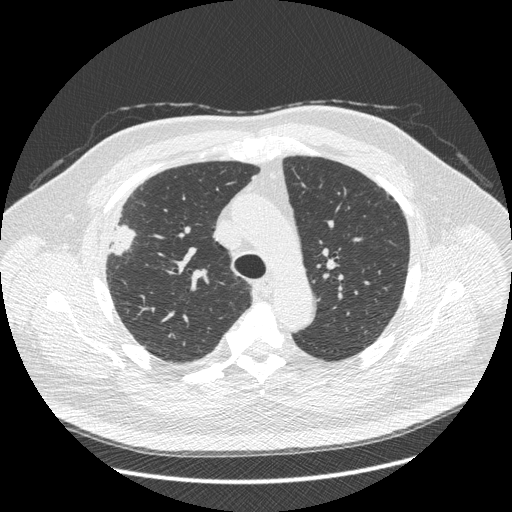
Chest CT (low-dose screening protocol), one axial image. Third screening round (two years after baseline). Lung window (W 1500 / L -600 HU). 1.25 mm slice thickness. Standard (soft-tissue) reconstruction kernel (STANDARD). Male, age 66 years at enrolment. Current smoker at enrolment.
• Expert reader's lesion annotation, bounding box [x1, y1, x2, y2] px = [87, 205, 147, 270].
• The exam's reader record, not a measurement of the box and not confirmed to be the same lesion: non-calcified nodule or mass ≥4 mm, right upper lobe, 48 × 25 mm, spiculated (stellate) margins, soft tissue attenuation, pre-existing on the prior screen: no.
• Official screen result: positive, other.
• Lung cancer was diagnosed 35 days after this screen: non-small cell carcinoma, right upper lobe, stage IV (AJCC 6th edition), 50 mm at pathology.